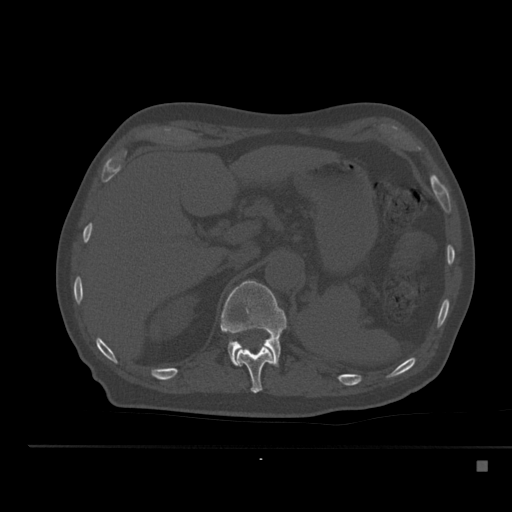
CT including the spine, one axial slice. Slice 239 of 517 in the series (ordered by position). Reconstruction kernel Br40s. 120 kVp. Bone window (W 1800 / L 400 HU). 1.5 mm slice thickness. 512 × 512 image matrix. Patient: male, 70 years. From the clinical record (not read from this slice): primary cancer: renal.
Outlined on this slice (semi-automatically segmented with operator editing):
- T11 vertebra: bounding box <236,347,273,393> (left, top, right, bottom; pixels)
- T12 vertebra: <220,280,288,366>